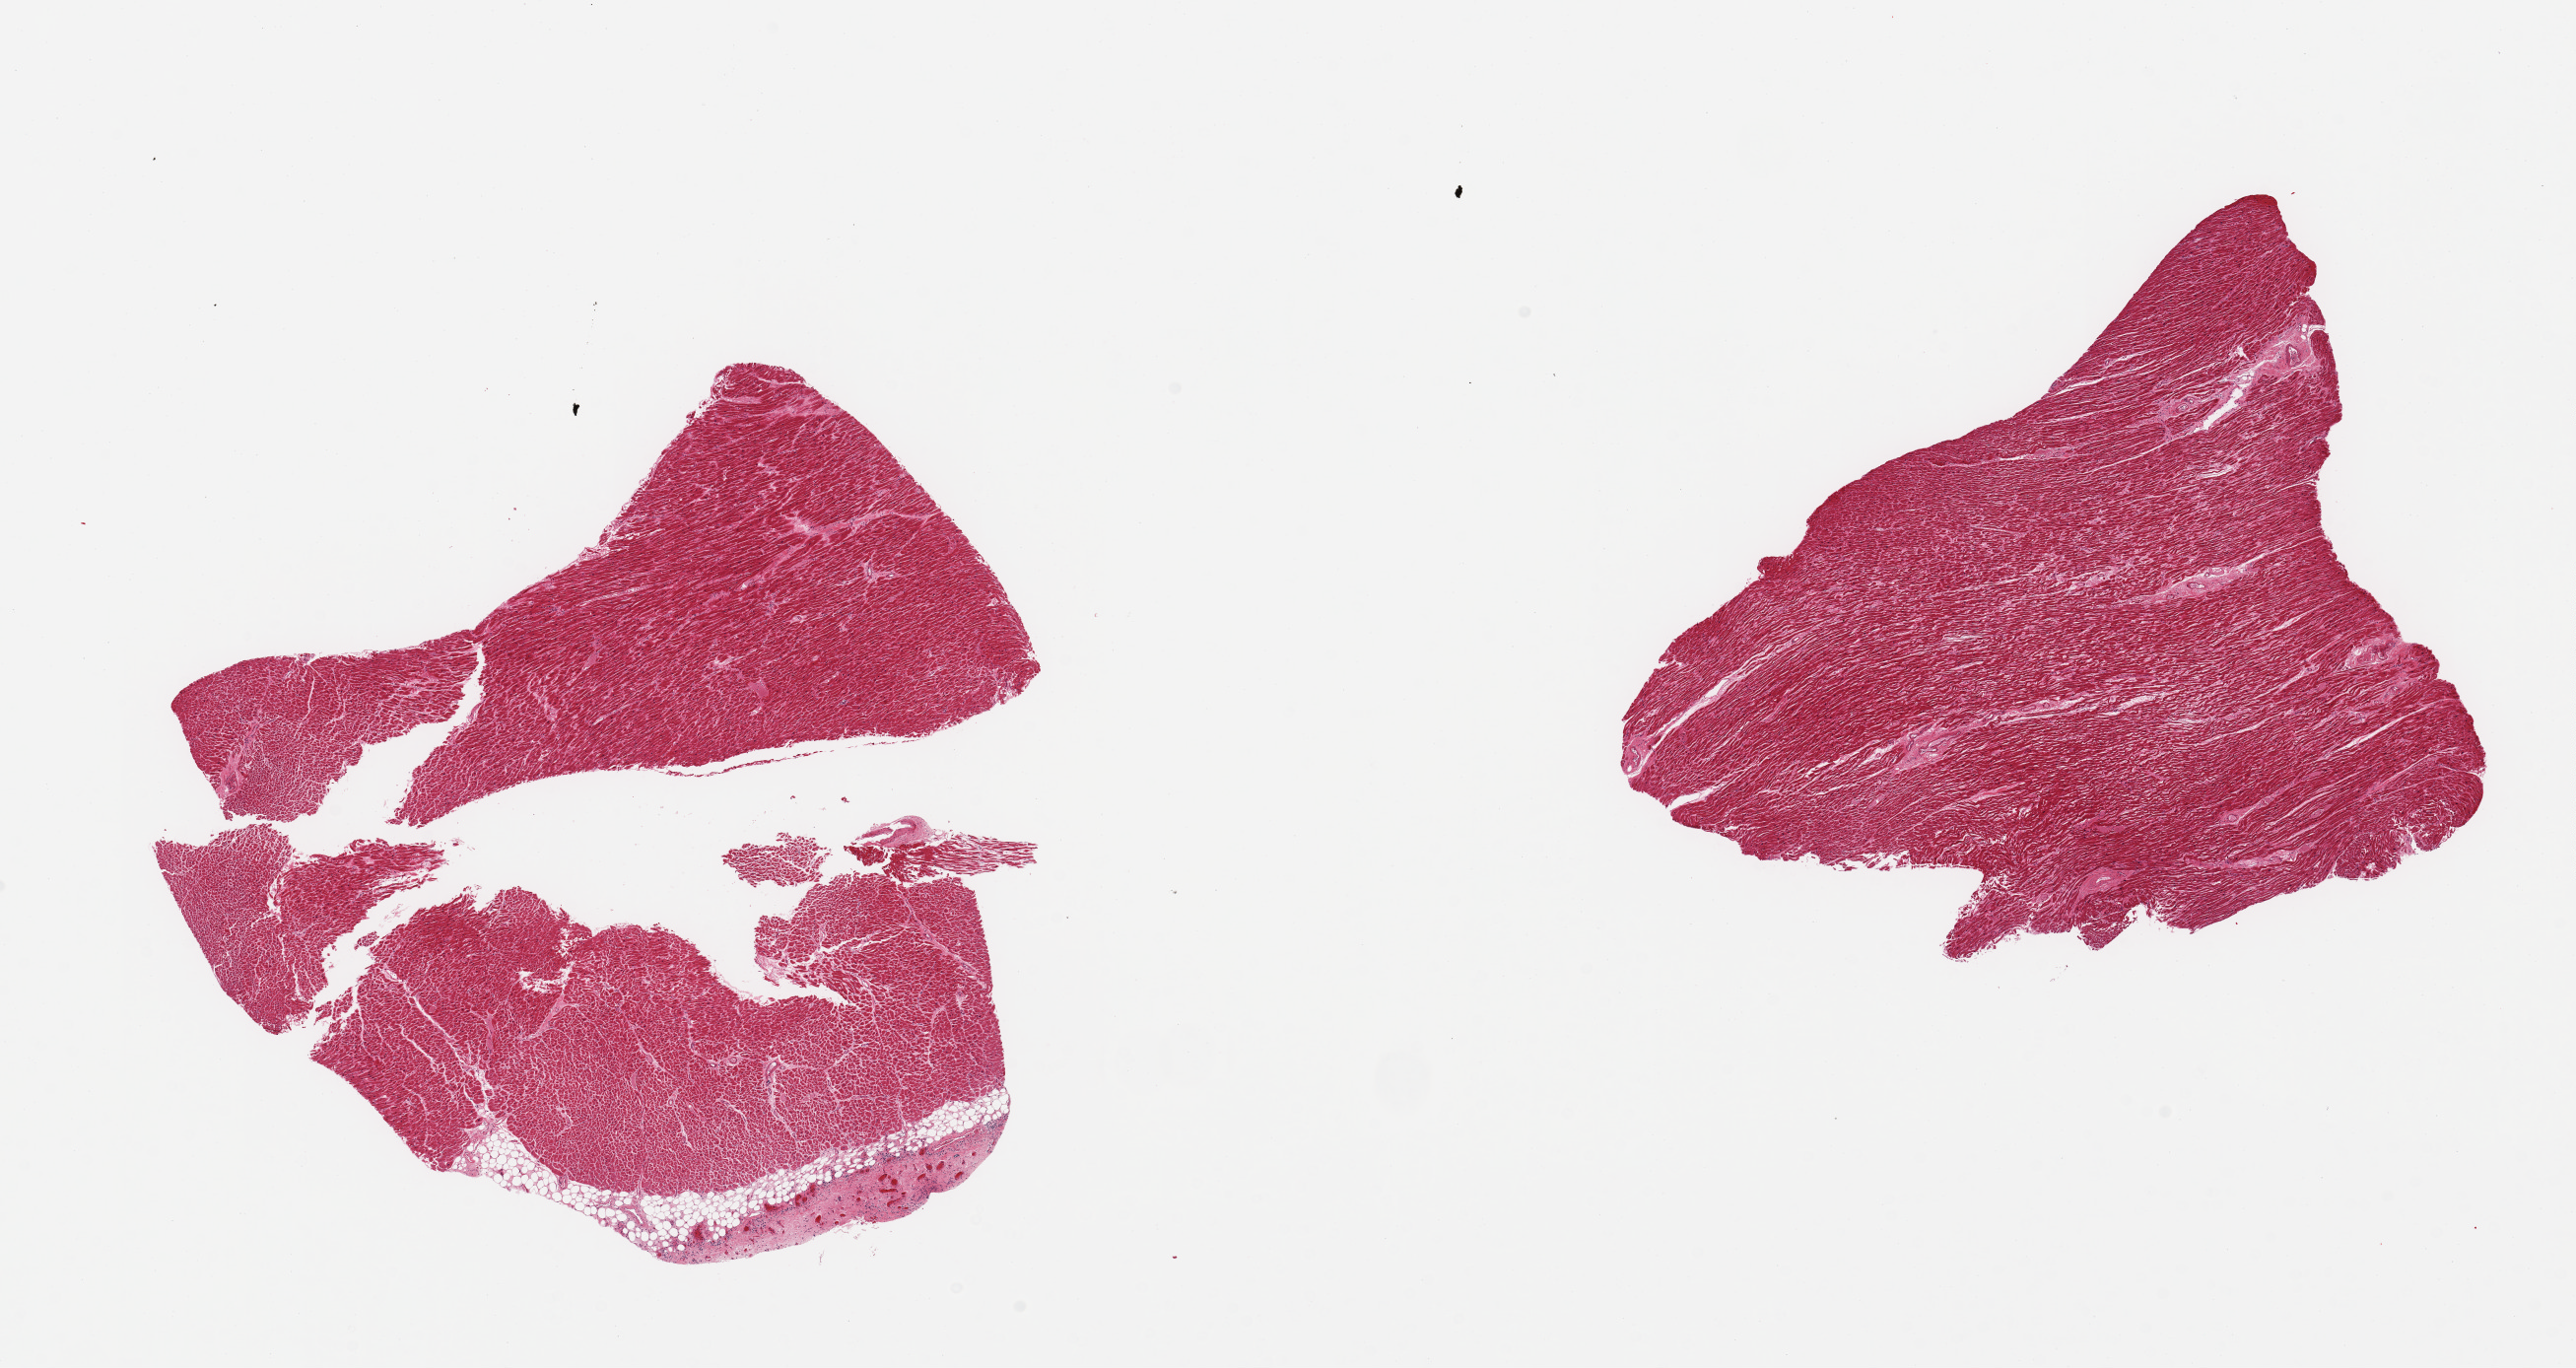
Whole-slide image, haematoxylin and eosin stain — low-resolution overview of the scanned area, about 20.7 x 11.0 mm. PAXgene-fixed paraffin-embedded (PFPE) section. Target tissue: heart. Donor tissue sample. Male donor.
- reviewer comment on this tissue sample: 2 pieces, moderate chronic ischemic changes